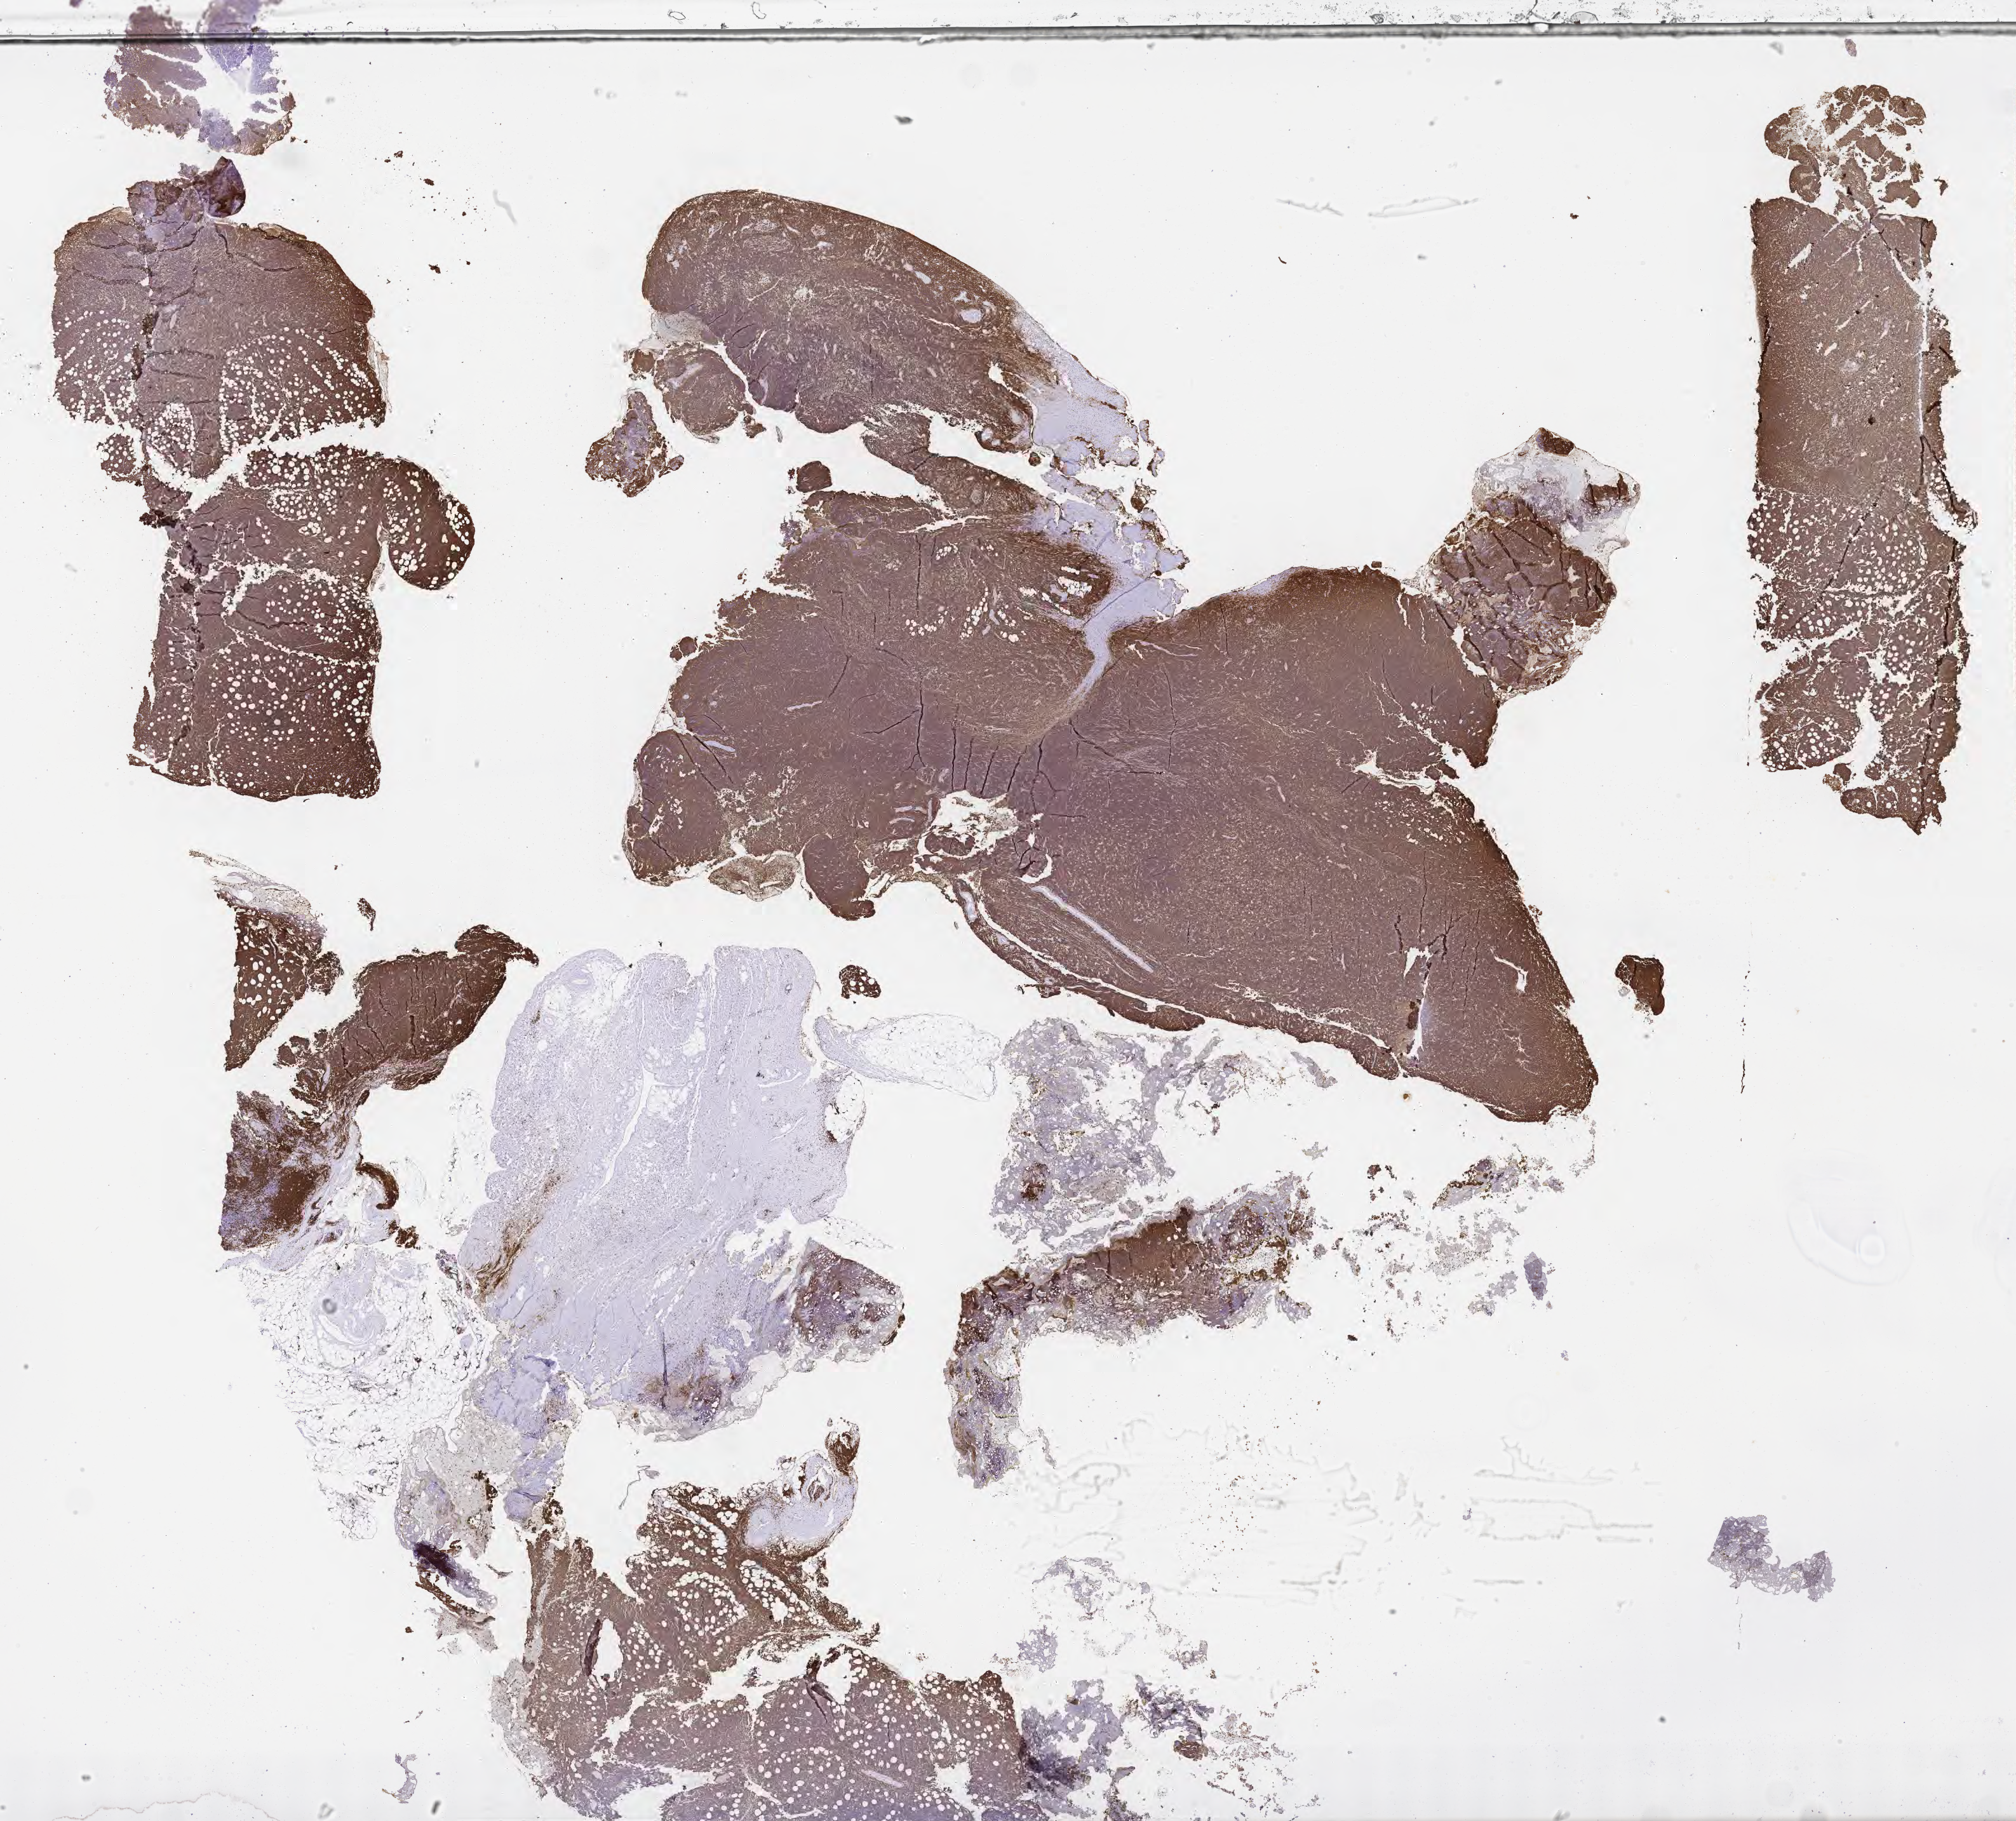
Whole-slide image, immunohistochemical stain for CD20 — whole scanned area (about 25.7 x 23.2 mm) shown as a low-resolution overview. Specimen: tumor tissue. Patient female; aged 72.
Histologic diagnosis: Burkitt lymphoma, NOS.